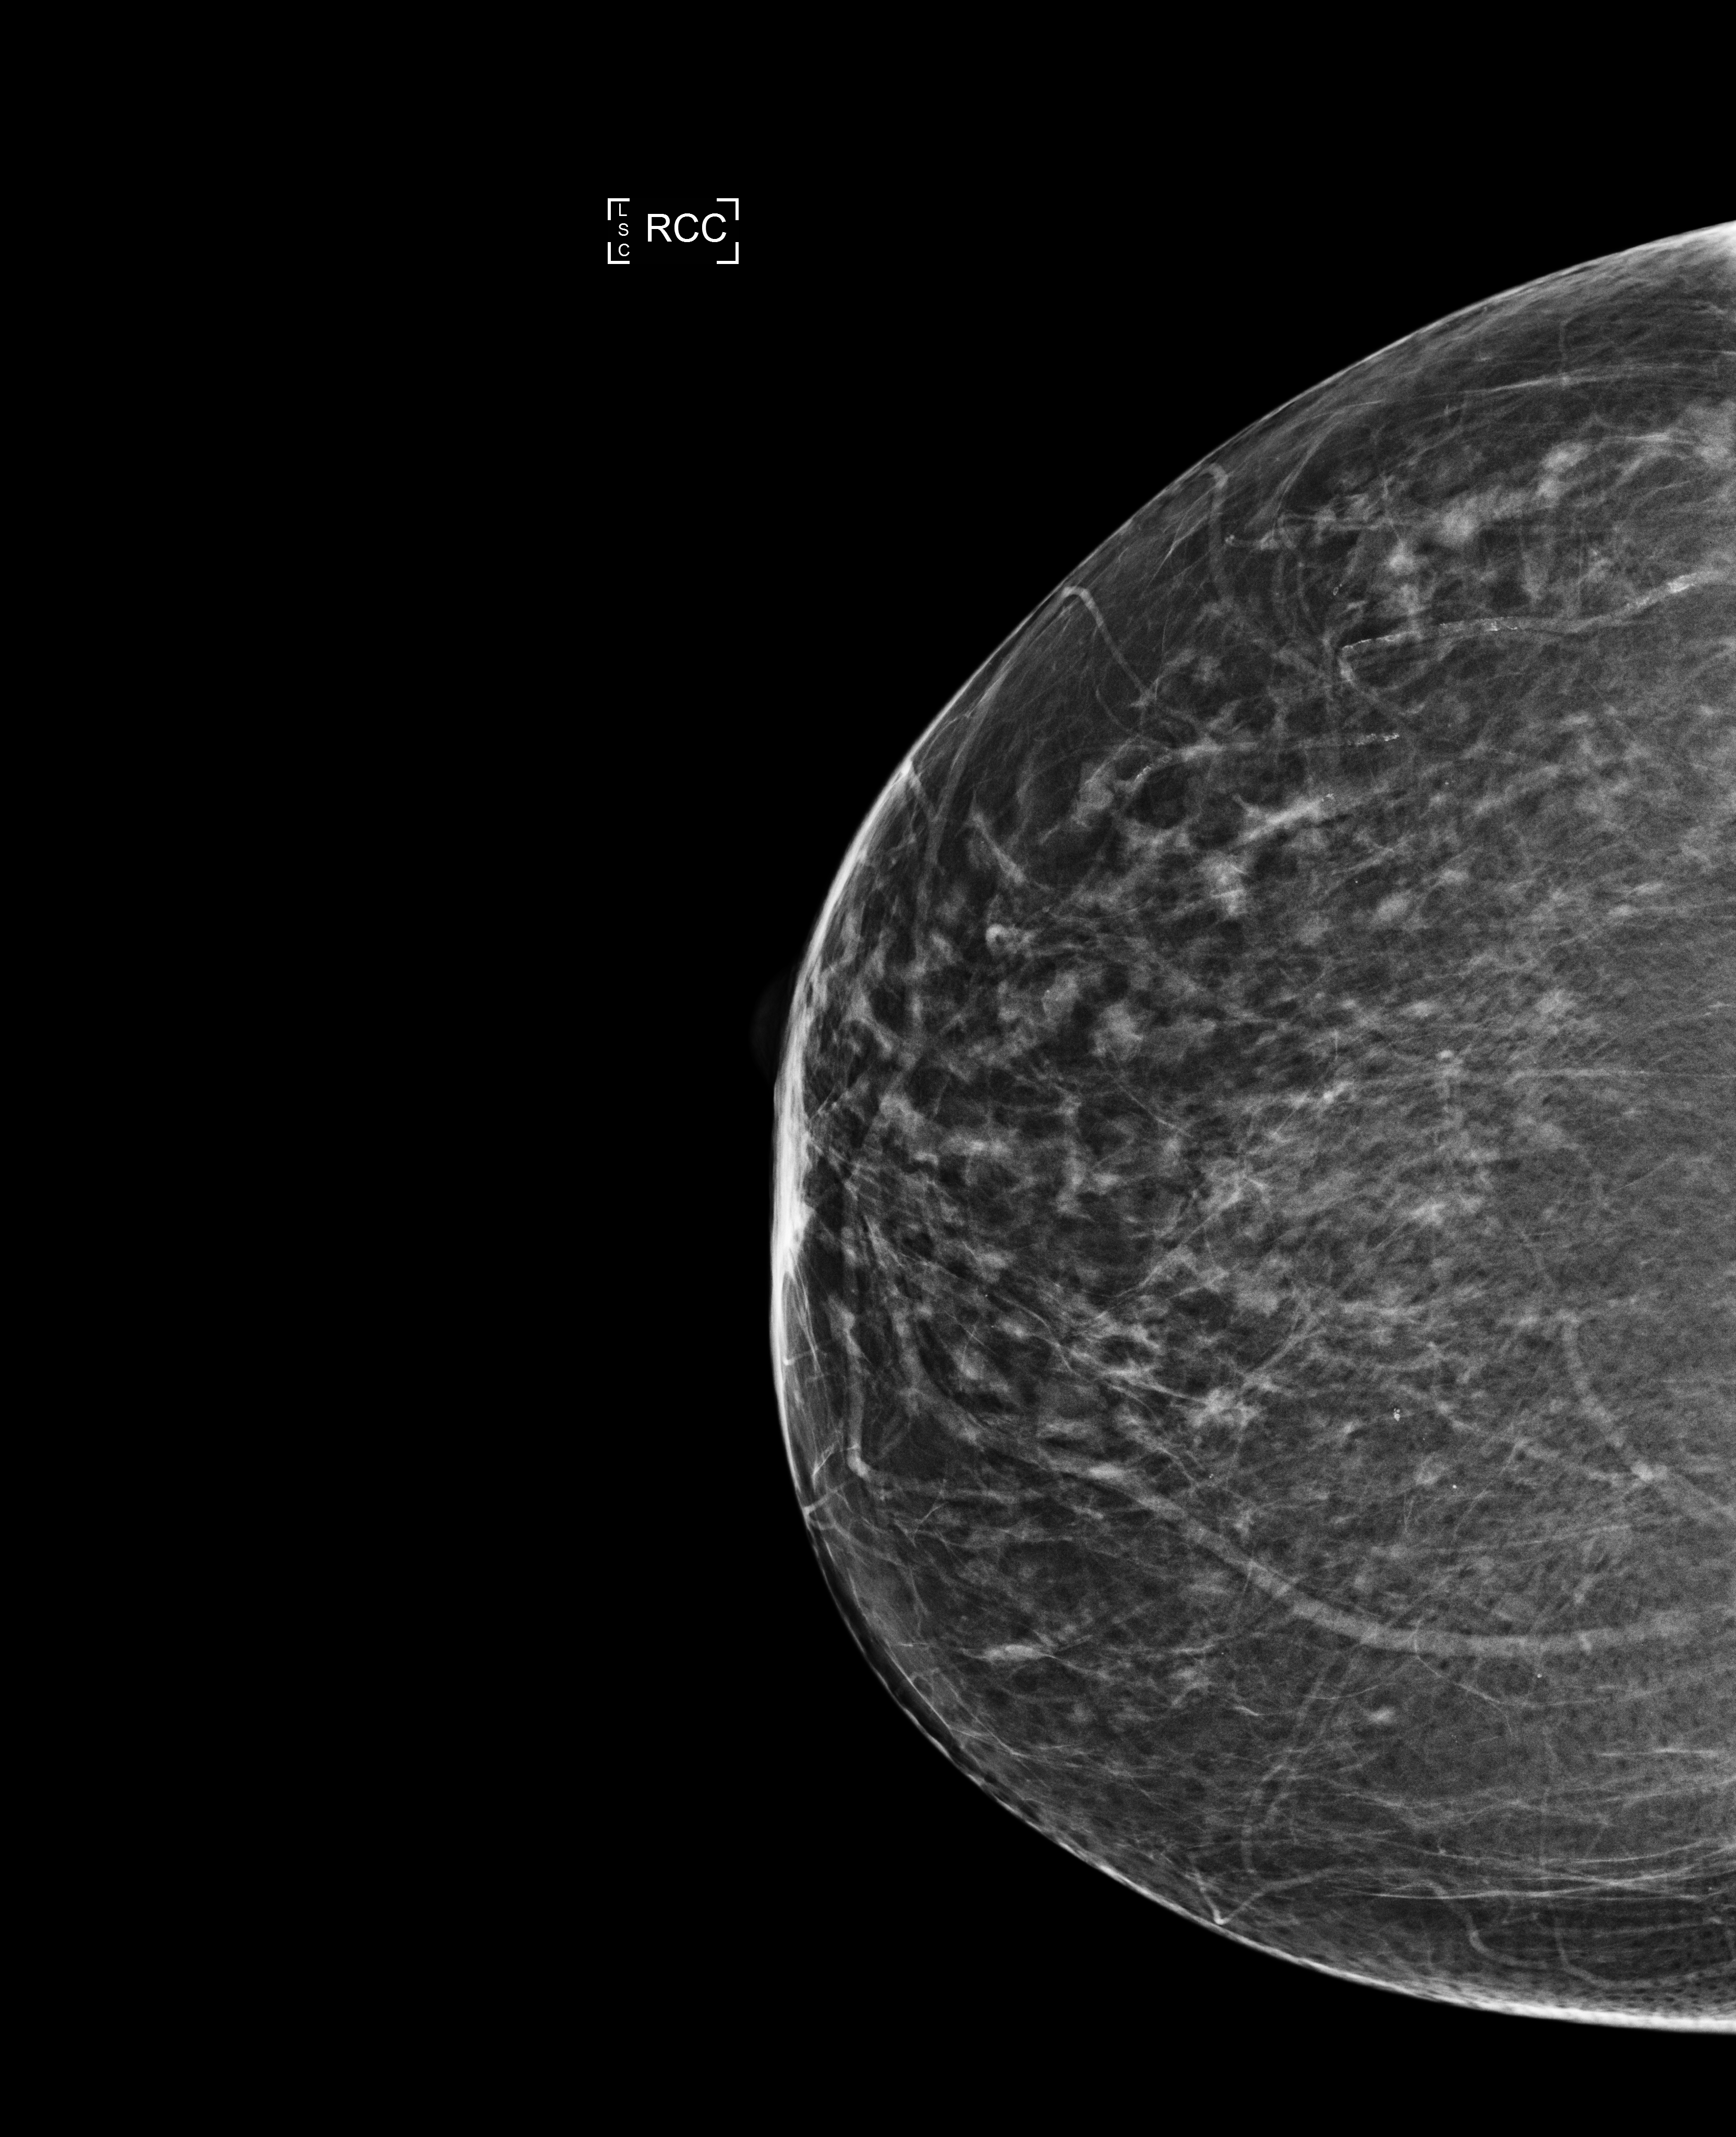
Digital mammogram (FFDM), right breast, cranio-caudal projection, screening examination, compressed breast thickness 60 mm. Patient: female, 73 years.
Breast density at the screening exam (both breasts): heterogeneously dense (BI-RADS density category c). Final BI-RADS assessment for this screening round (tomosynthesis exam, both breasts): category 1. Recall: no recall after this screen.